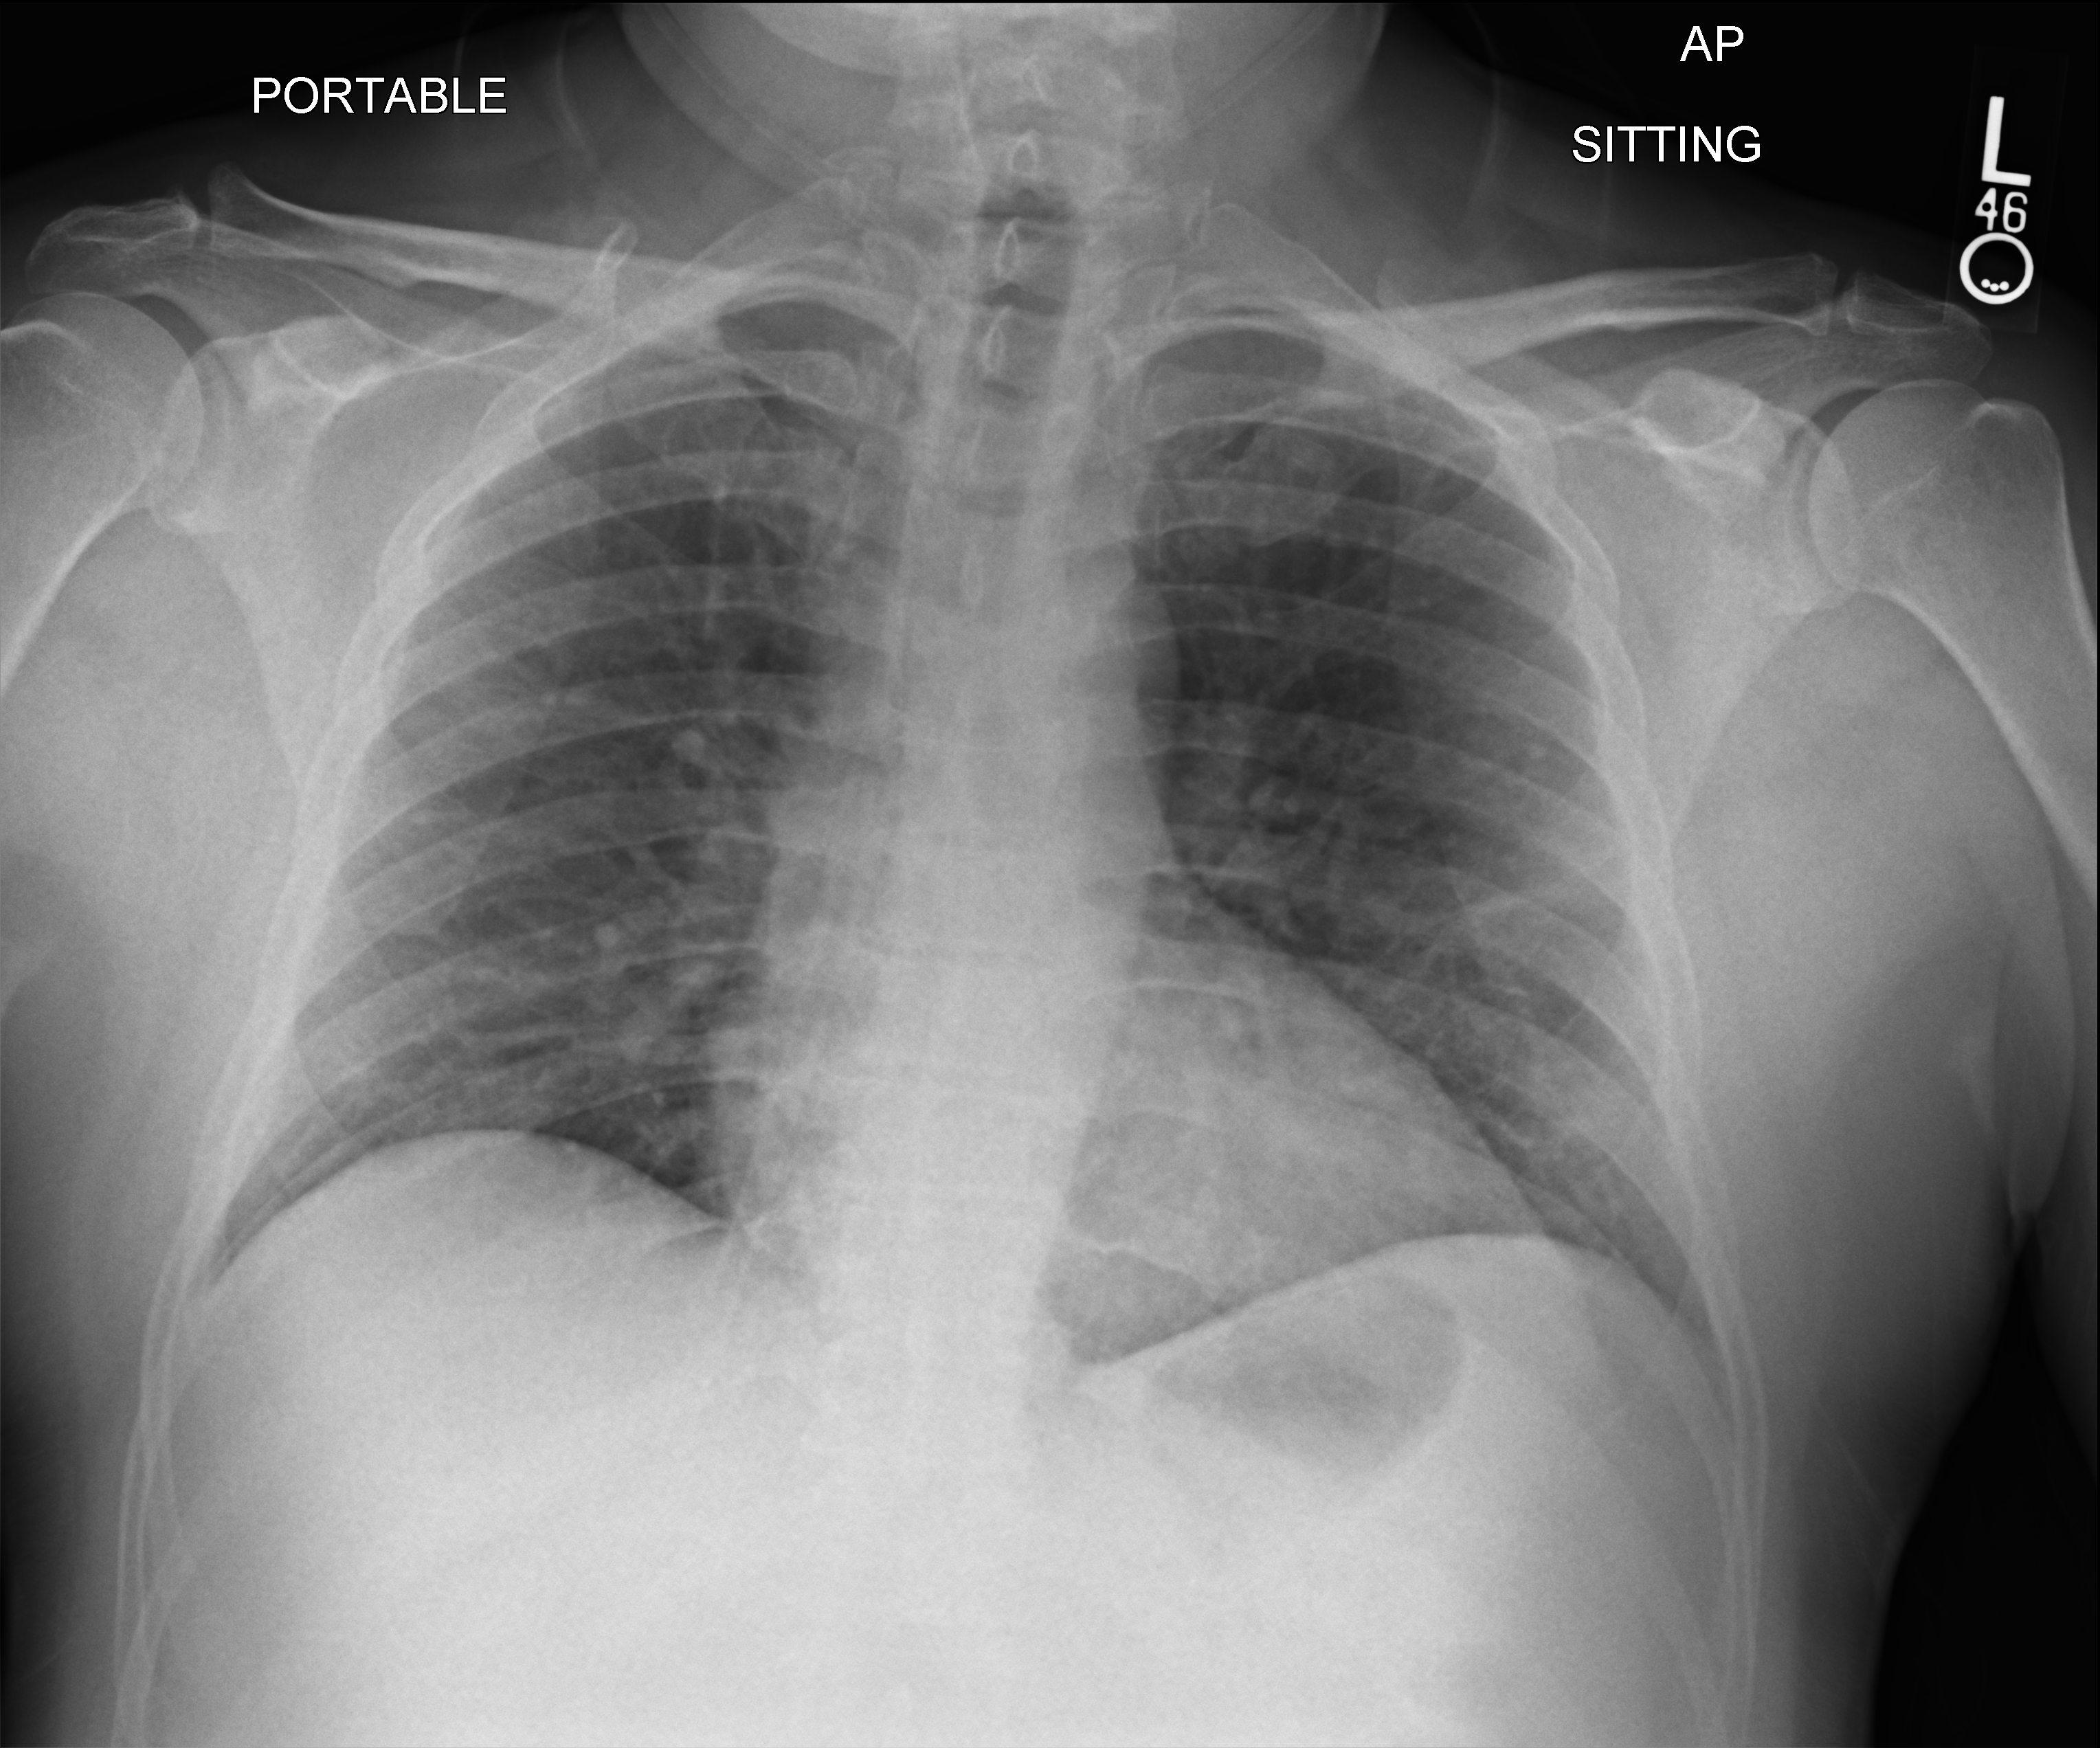
Portable chest radiograph, anteroposterior (AP) projection. Patient hospitalised with COVID-19; male, aged 18–59 years.
Hospital-stay facts (about this admission, not read from this image; timing relative to this image not recorded):
- mechanically ventilated during this hospital stay: yes
- admitted to intensive care during this hospital stay: yes